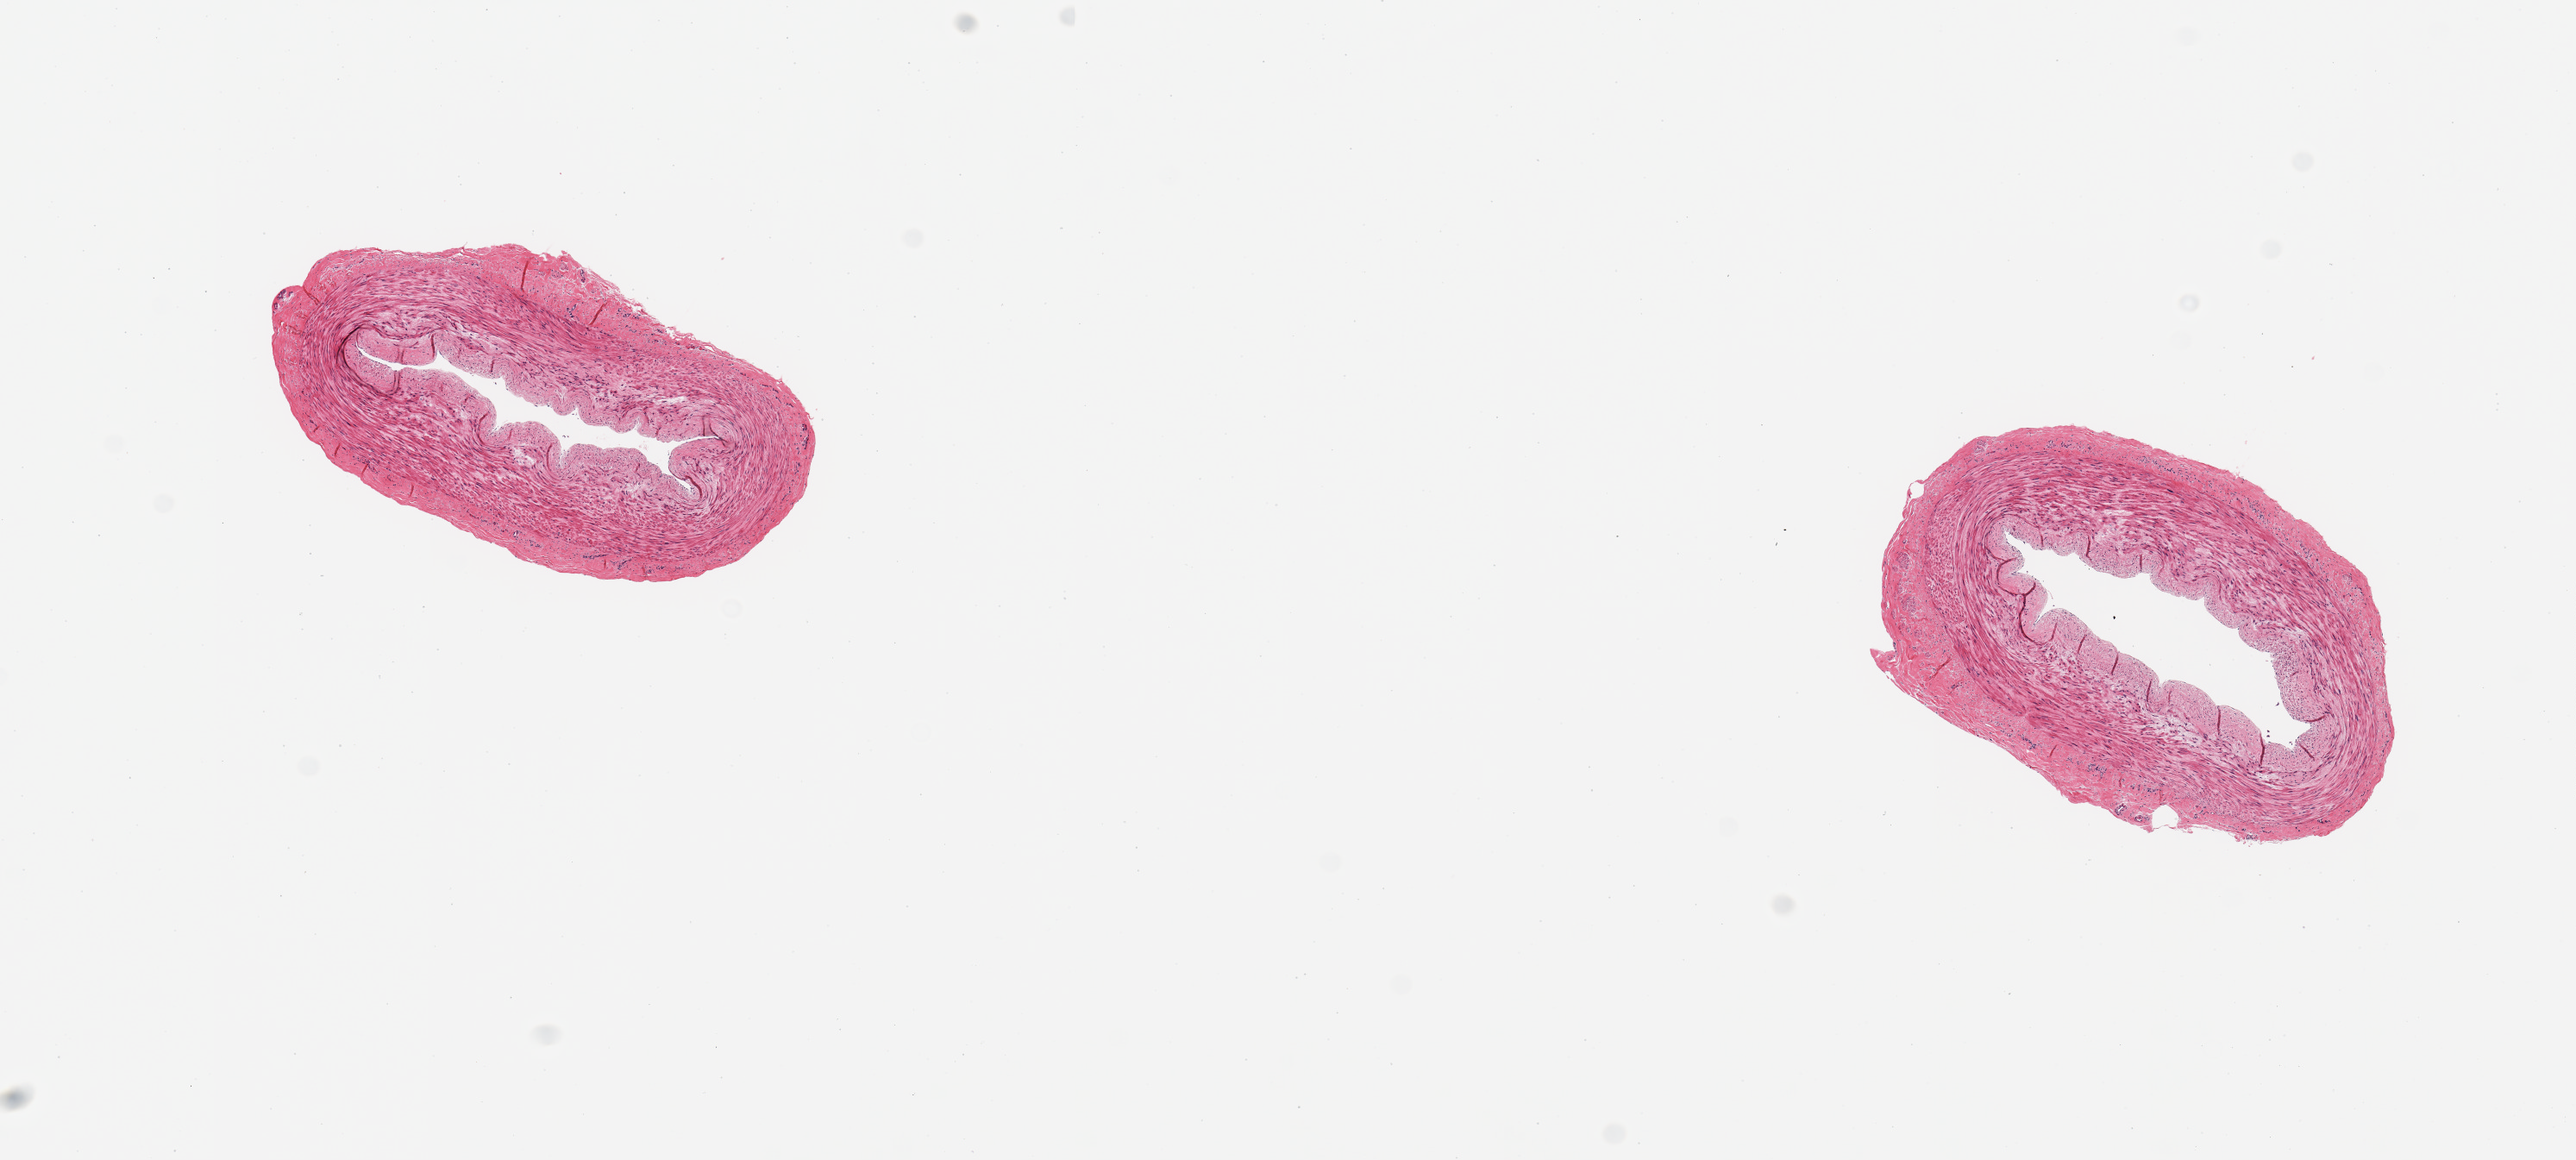
Digitized H&E-stained section, low-resolution overview of the scanned area, about 11.8 x 5.3 mm, PAXgene-fixed, paraffin-embedded tissue, target tissue: tibial artery, tissue donor sample.
Review note (as recorded): 2 pieces, no atherosis, no adherent fat.